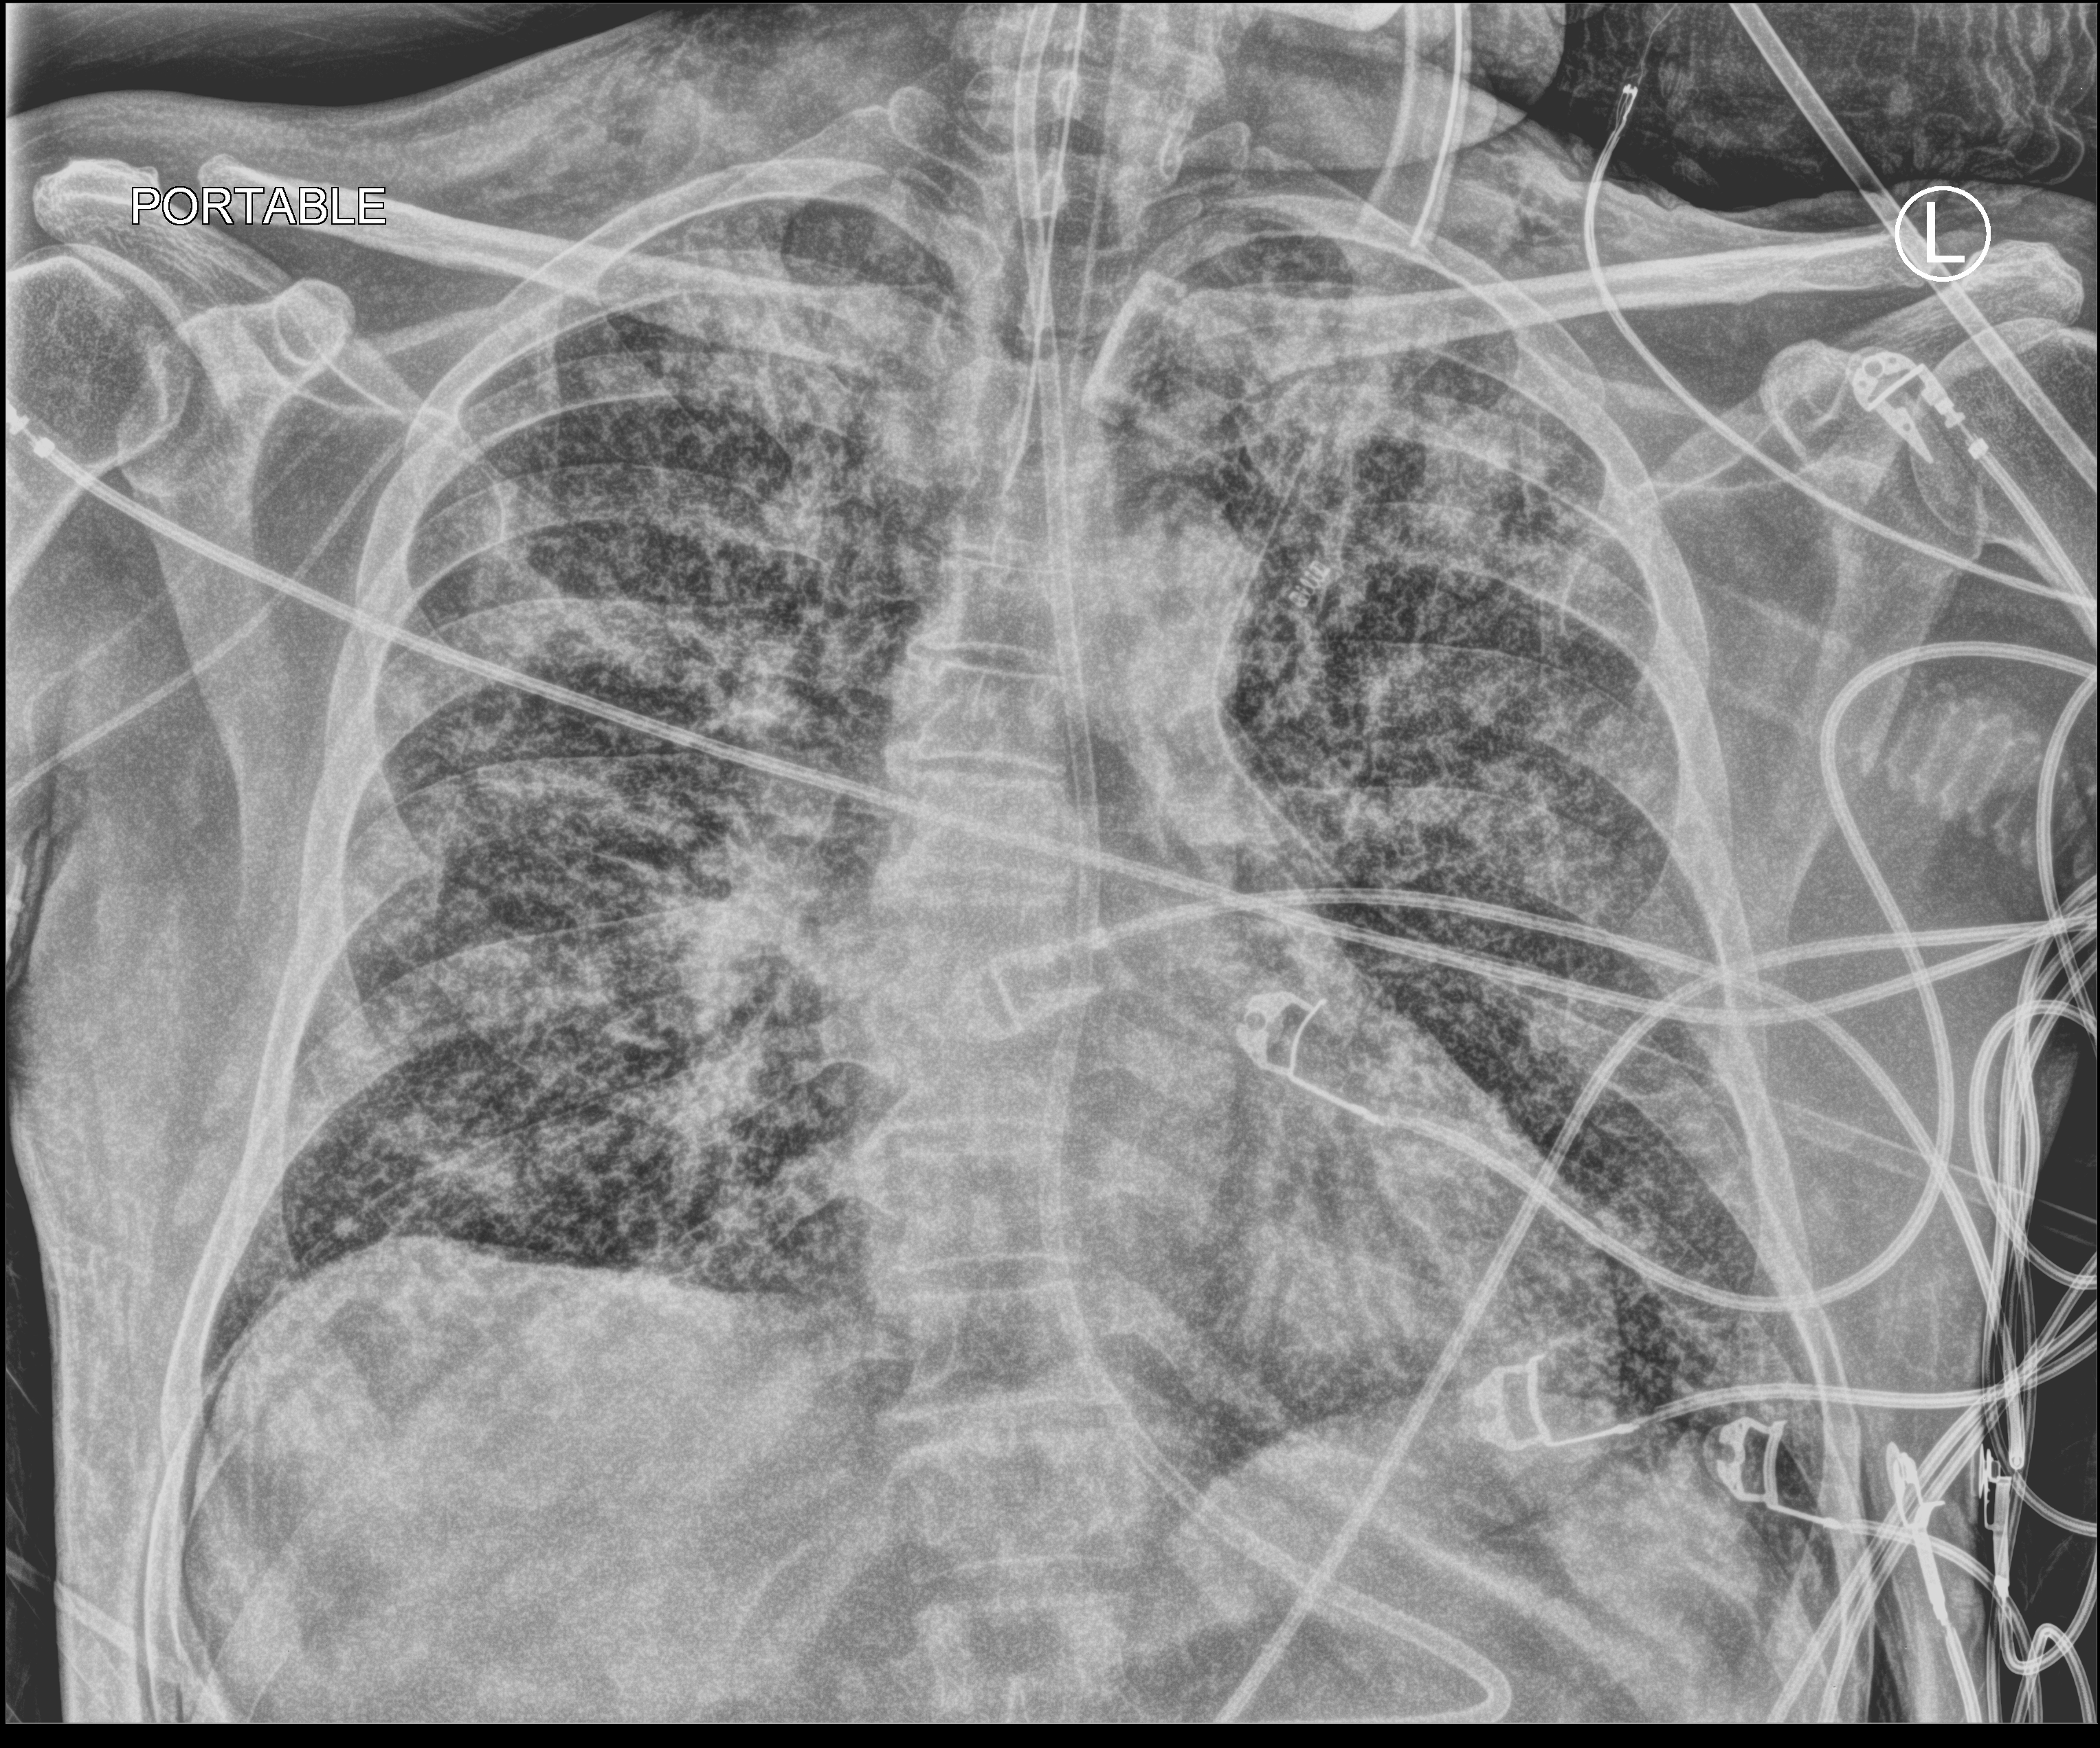
Chest X-ray (portable); anteroposterior (AP) projection. Patient hospitalised with COVID-19; male, aged 18–59 years.
Admission-level facts for this patient (not findings on this image; timing relative to this image not recorded): length of hospital stay: 42 days.